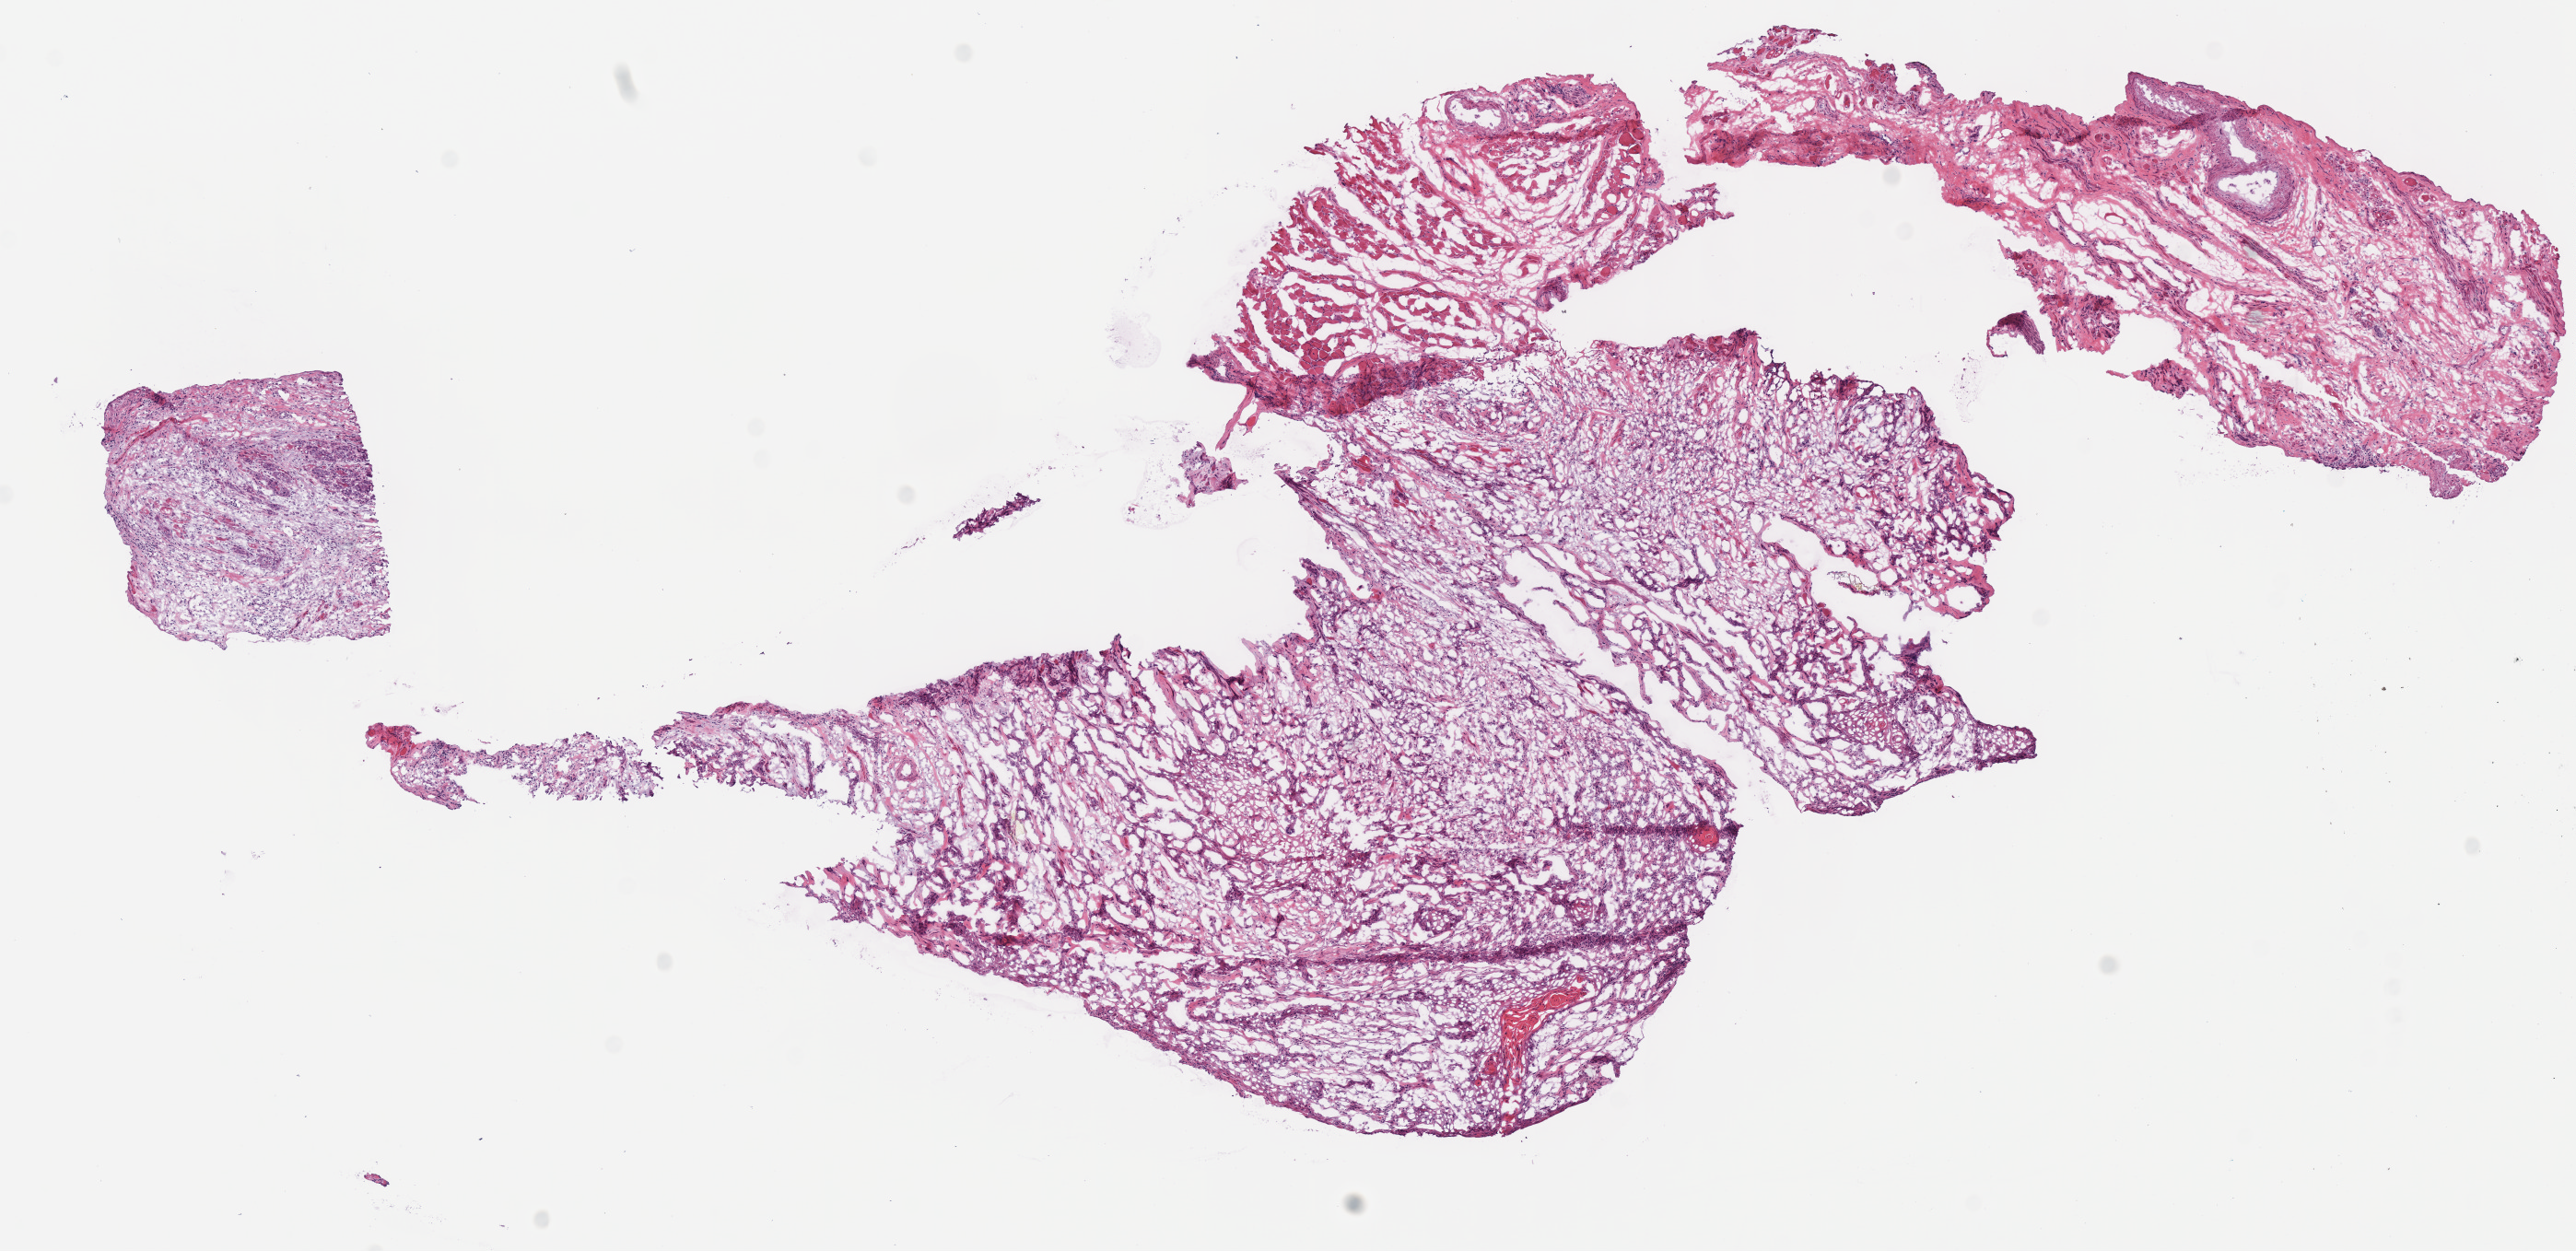
Digitized Hematoxylin and eosin (H&E) stained tissue section (whole slide), shown as a low-resolution overview of the whole scanned area (about 11.0 x 5.4 mm, acquisition: 40x scan). Frozen section. Head and neck, primary tumour sample. Female, age 87 years at initial diagnosis. Pathologist review of this section (percent, as recorded): tumour cells 65%, tumour nuclei 65%.
Histologic diagnosis: Squamous cell carcinoma, NOS (tongue, NOS).